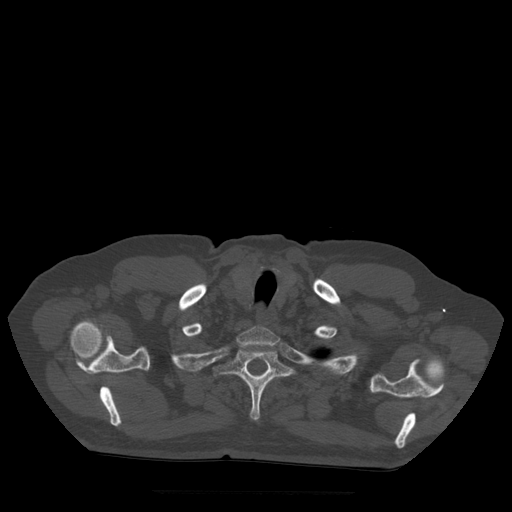
CT including the spine, one axial slice; position 428 of 522 along the scan axis; bone window (W 1800 / L 400 HU); 1.25 mm slice thickness; 512 × 512 image matrix. Patient age 72 years. From the clinical record (not read from this slice): primary cancer: prostate.
Annotated regions visible in this slice (semi-automatically segmented with operator editing):
- T1 vertebra: bounding box [x1, y1, x2, y2] px = [237, 327, 280, 349]
- T2 vertebra: [214, 348, 294, 421]